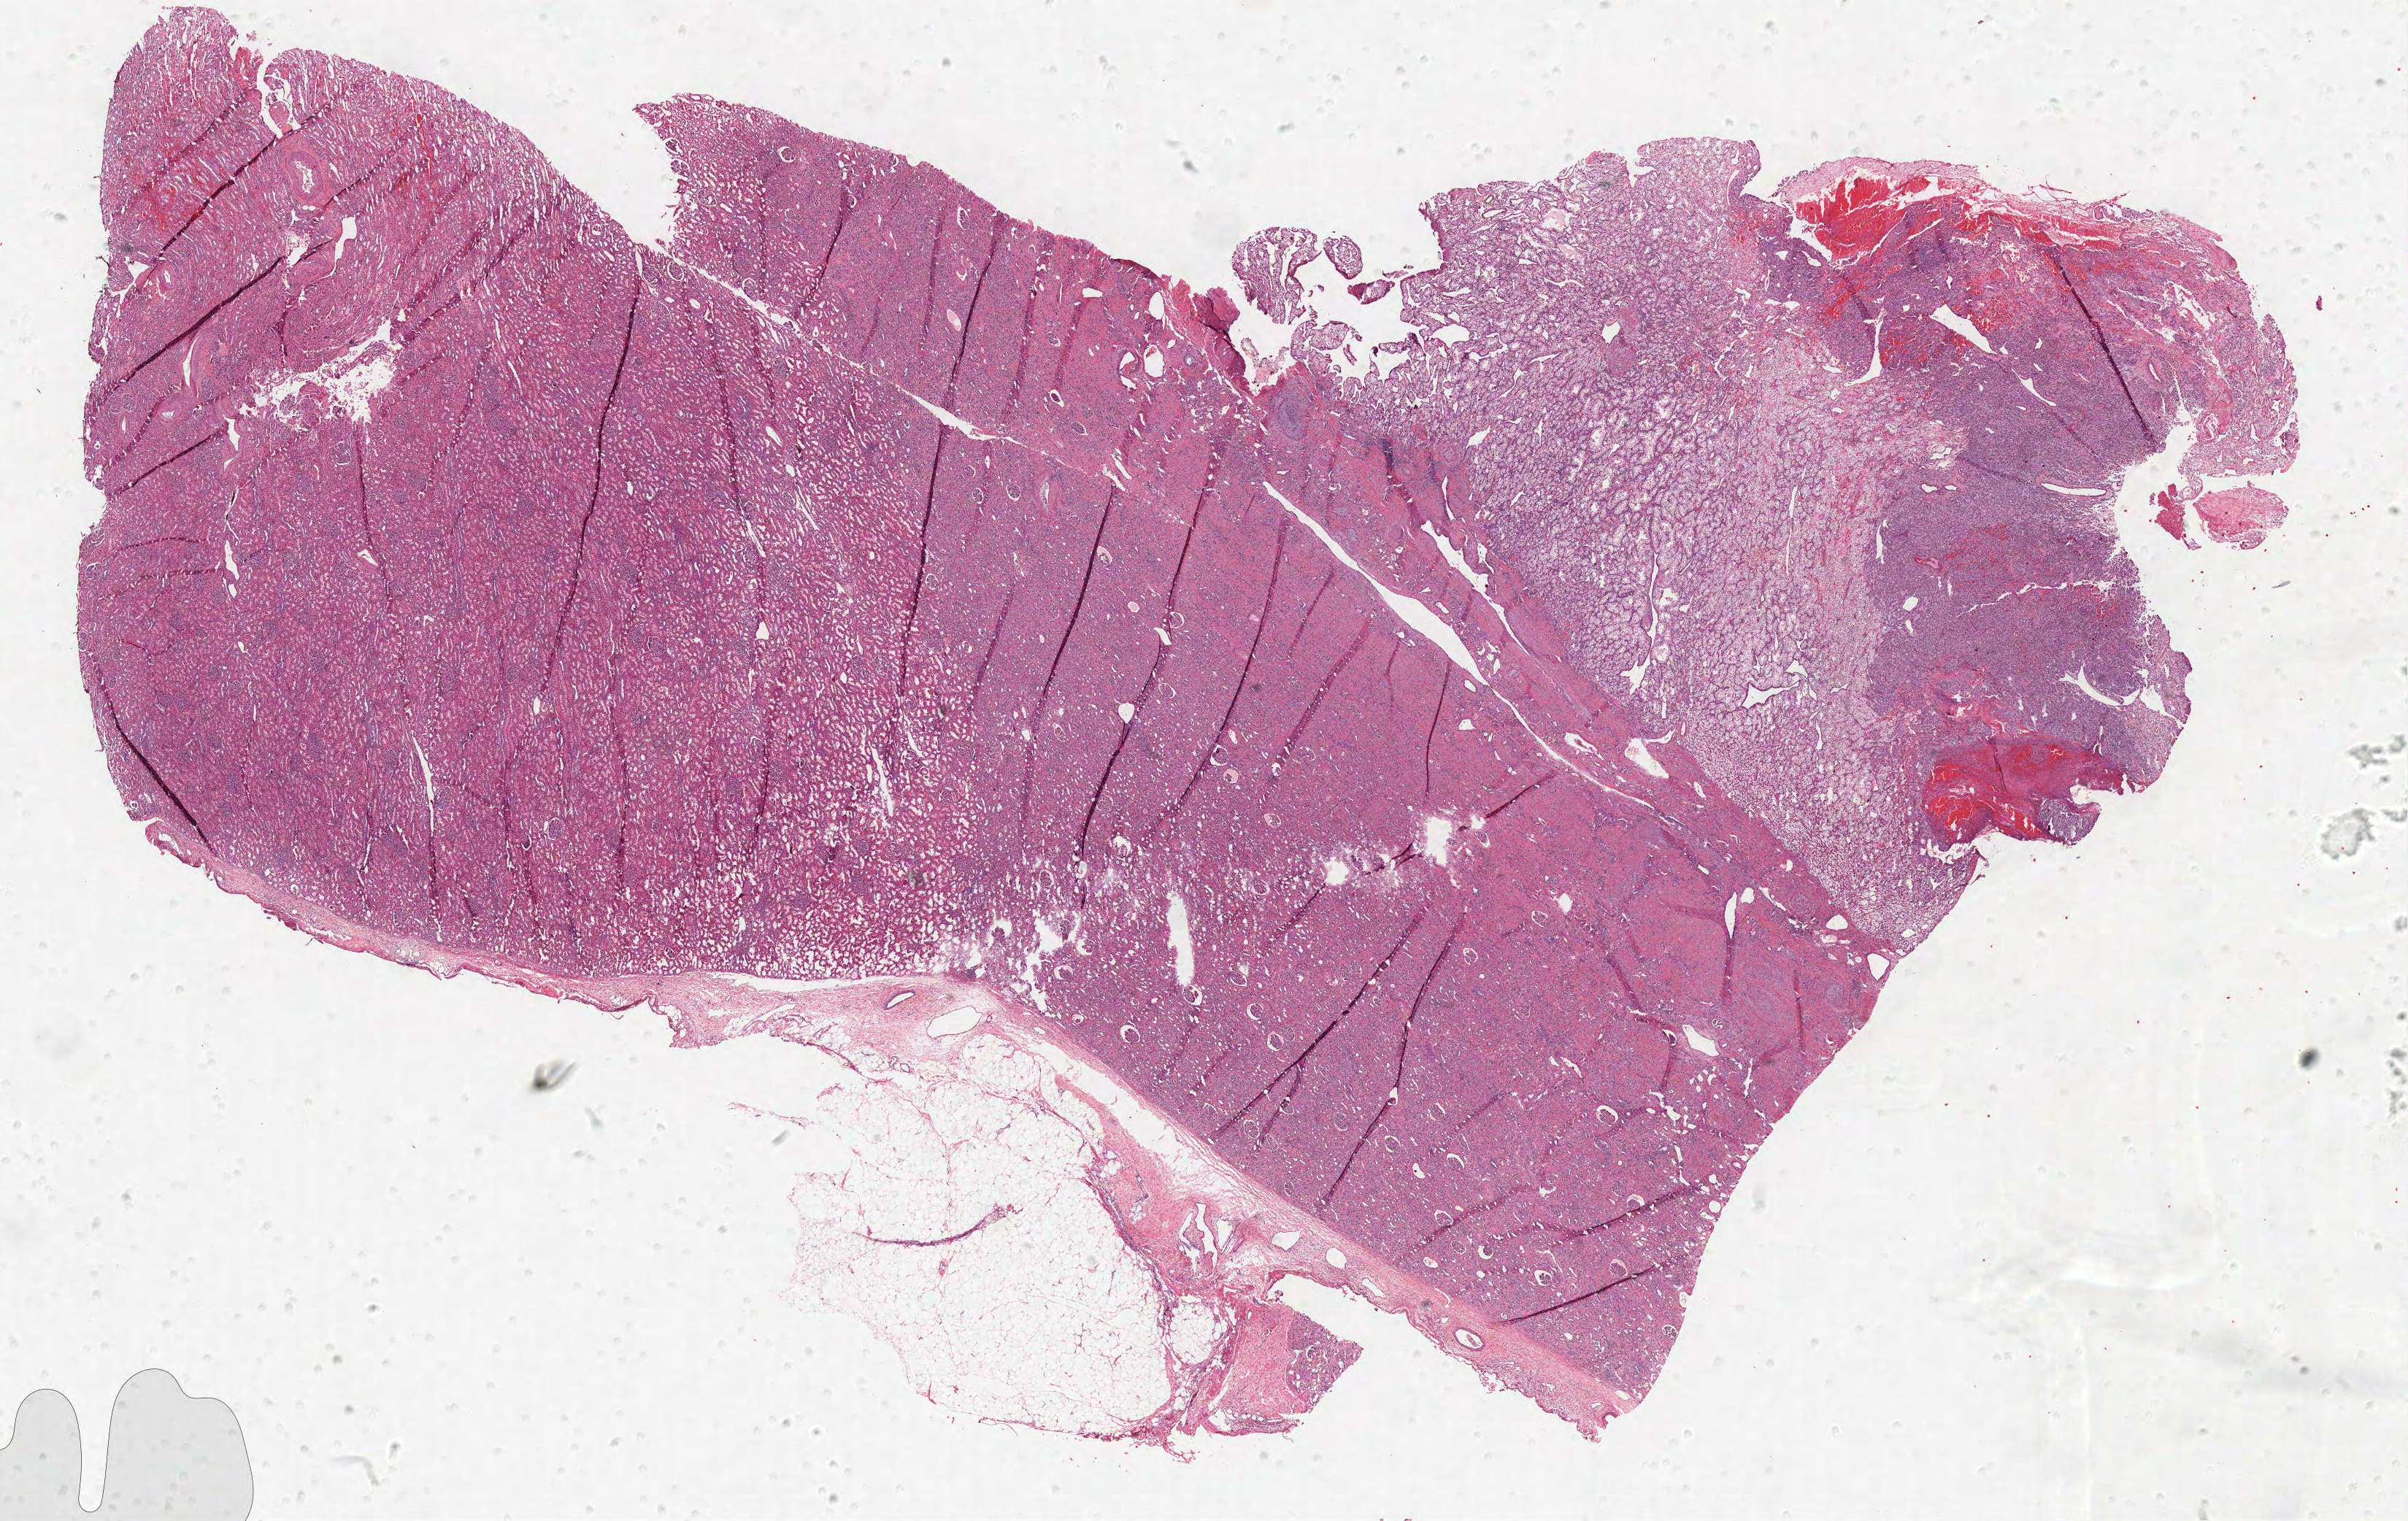
Digitized Hematoxylin and eosin (H&E) stained tissue section (whole slide) — low-resolution overview of the scanned area, about 26.4 x 16.7 mm; formalin-fixed paraffin-embedded (FFPE) diagnostic section; kidney, primary tumour sample. Female, age 53 years at initial diagnosis. Histologic grade: G2 (moderately differentiated).
* TNM: T1b N0 M0
* AJCC pathologic stage: I
* lymph nodes positive (case pathology): 0 of 3 examined
* diagnosis: Clear cell adenocarcinoma, NOS